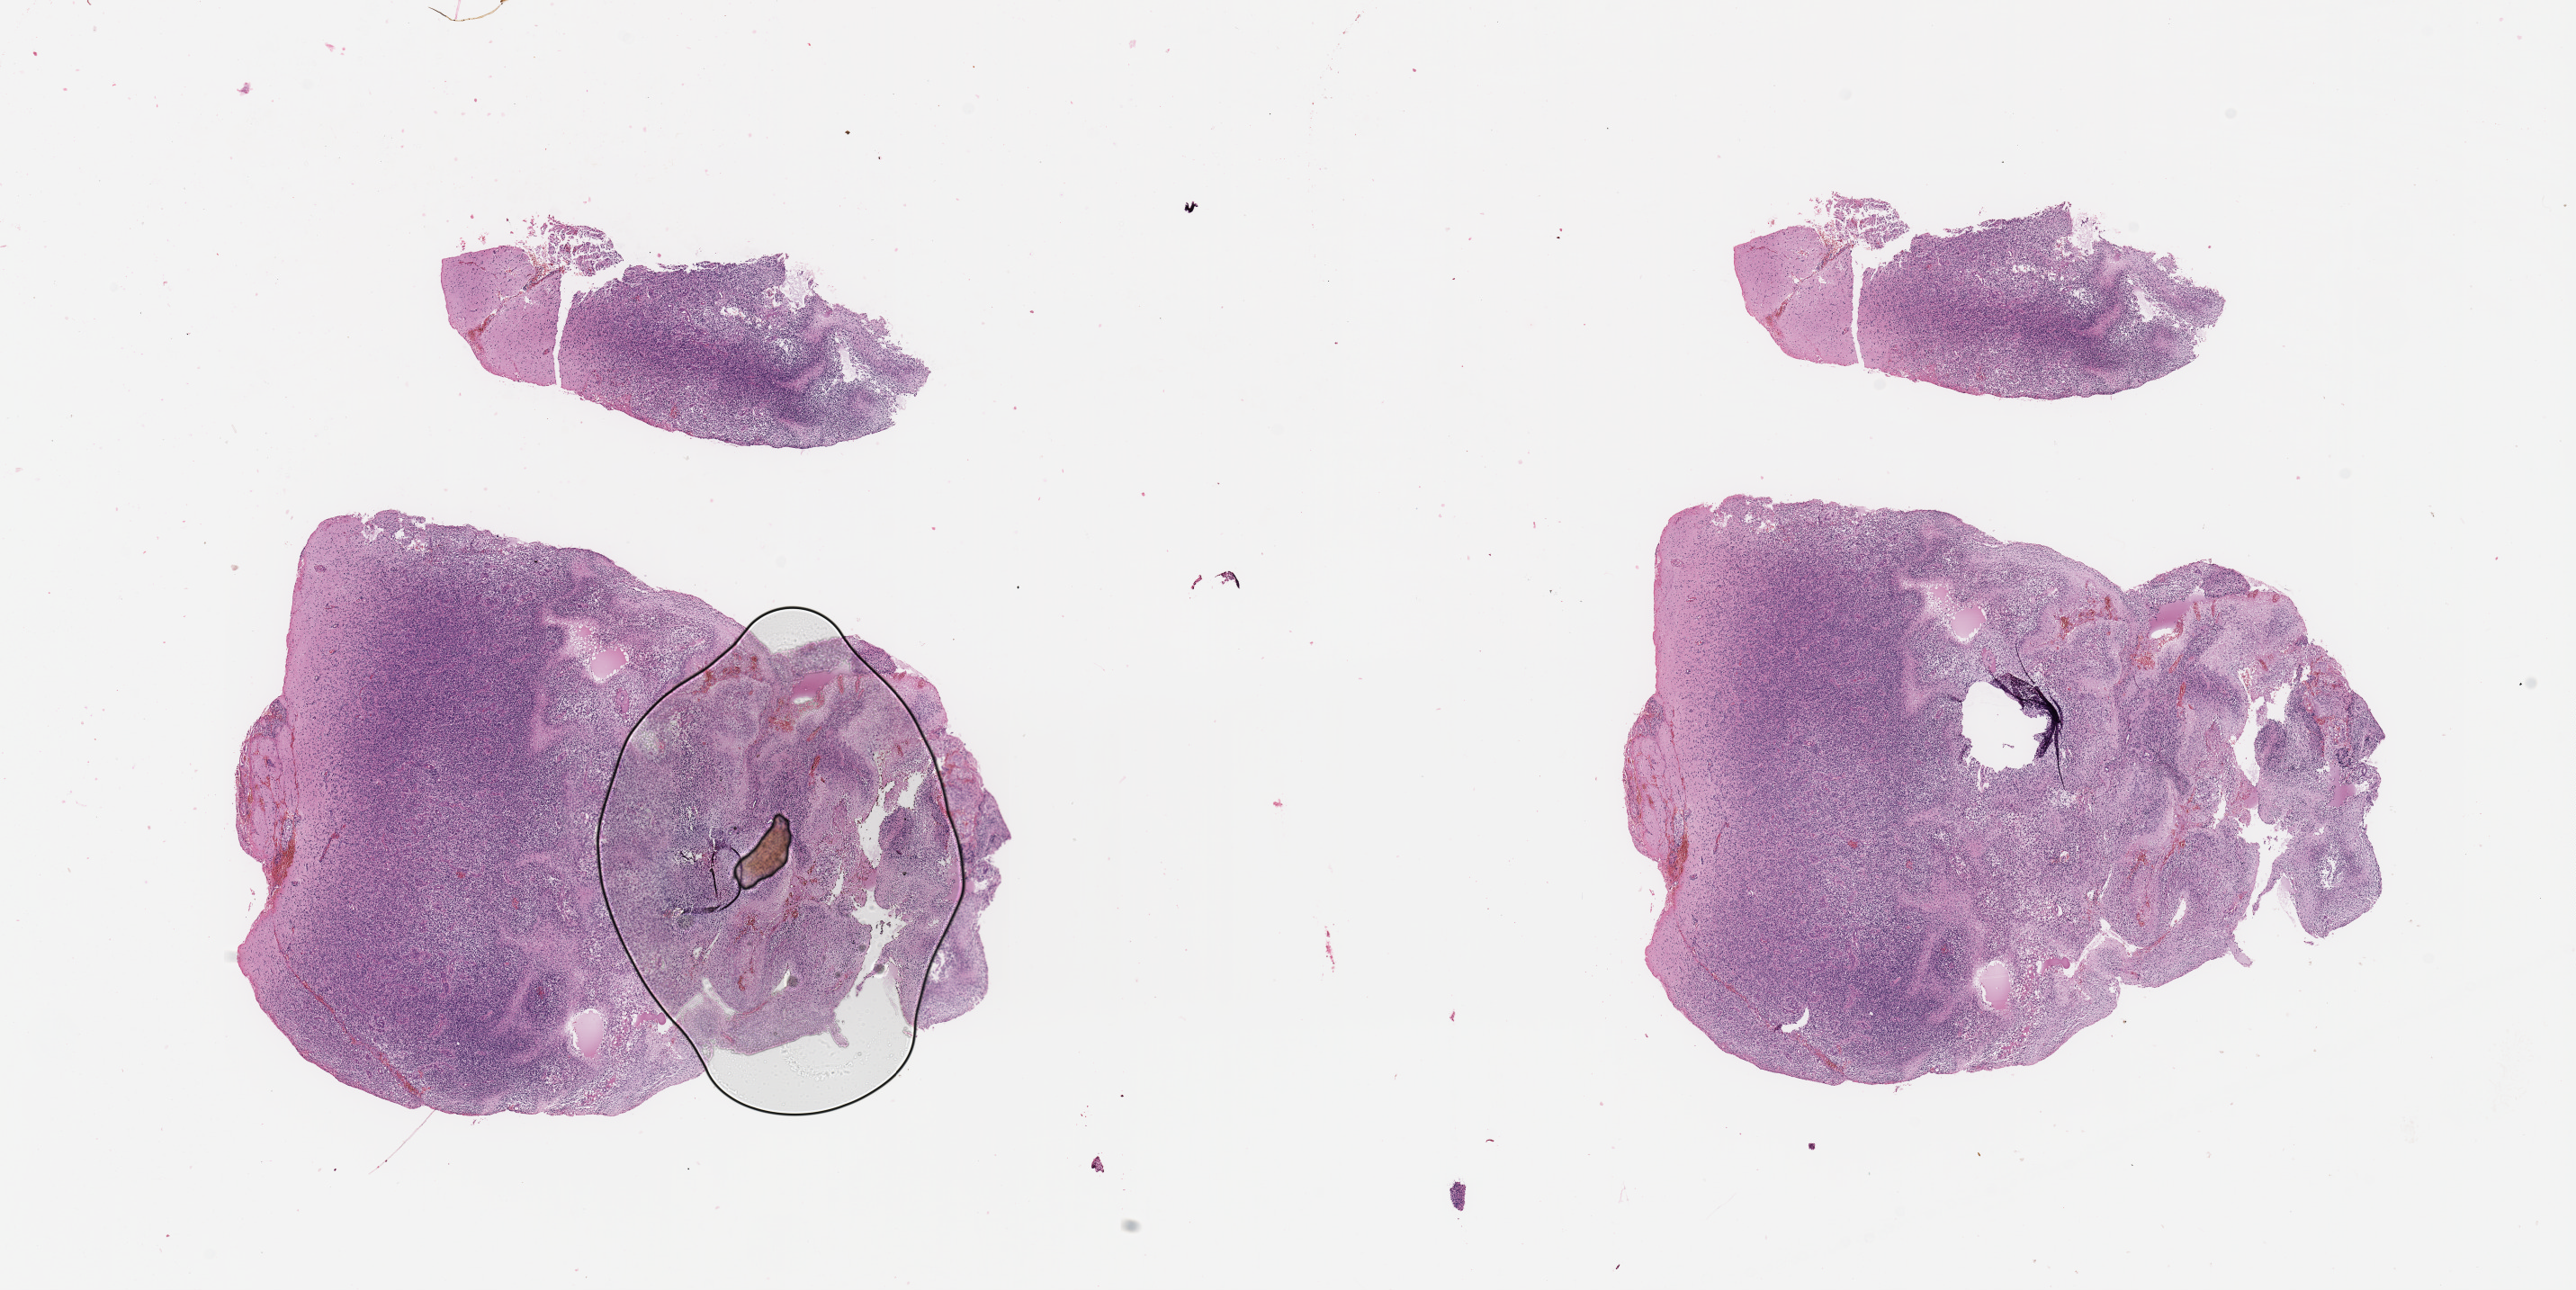
H&E-stained whole-slide image — whole scanned area (about 22.6 x 11.3 mm) shown as a low-resolution overview, tumour tissue sample, brain. Patient: female, age 68 years.
Histologic diagnosis: Glioblastoma. Primary tumour site (as recorded): parietal lobe.